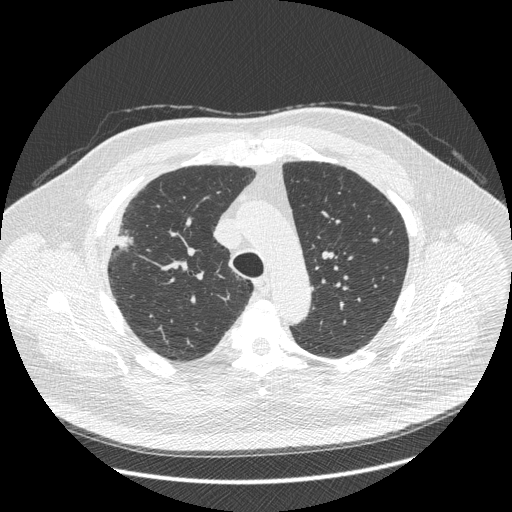
Low-dose screening chest CT, axial slice; third screening round (two years after baseline); lung window (W 1500 / L -600 HU); 1.25 mm slice thickness; 512 × 512 image matrix, field of view 400 × 400 mm. Male, age 66 years at enrolment. Current smoker at enrolment.
Expert reader's lesion annotation, bounding box <88,211,148,271> (left, top, right, bottom; pixels). Reader record for this screening exam (exam-level; its link to the box is not recorded): non-calcified nodule or mass ≥4 mm, right upper lobe, 48 × 25 mm, spiculated (stellate) margins, soft tissue attenuation, pre-existing on the prior screen: no. Lung cancer was diagnosed 35 days after this screen: non-small cell carcinoma, right upper lobe, stage IV (AJCC 6th edition), 50 mm at pathology.